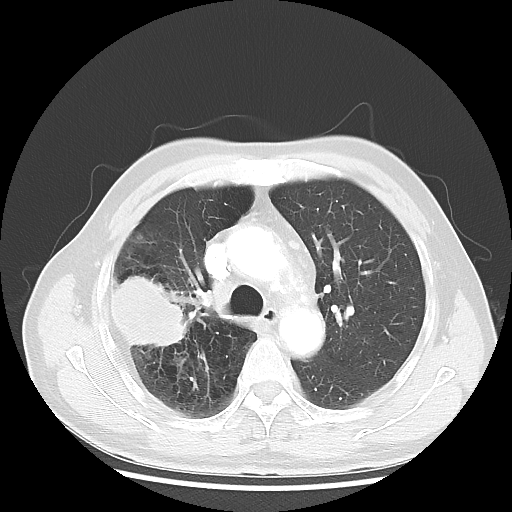
Chest CT, one axial slice. Position 34 of 50 along the scan axis. Reconstruction kernel LUNG. 120 kVp. Lung window (W 1500 / L -600 HU). 5 mm slice thickness. 512 × 512 image matrix. Male patient, age 69 years. From the clinical record (not read from this slice): clinical TNM (as recorded): T3 N0 M0; histopathological grade: G3.
Annotated regions visible in this slice (bounding box drawn by a radiologist):
- lung tumour (recorded histology: adenocarcinoma): box from (x=110, y=267) to (x=193, y=354) px